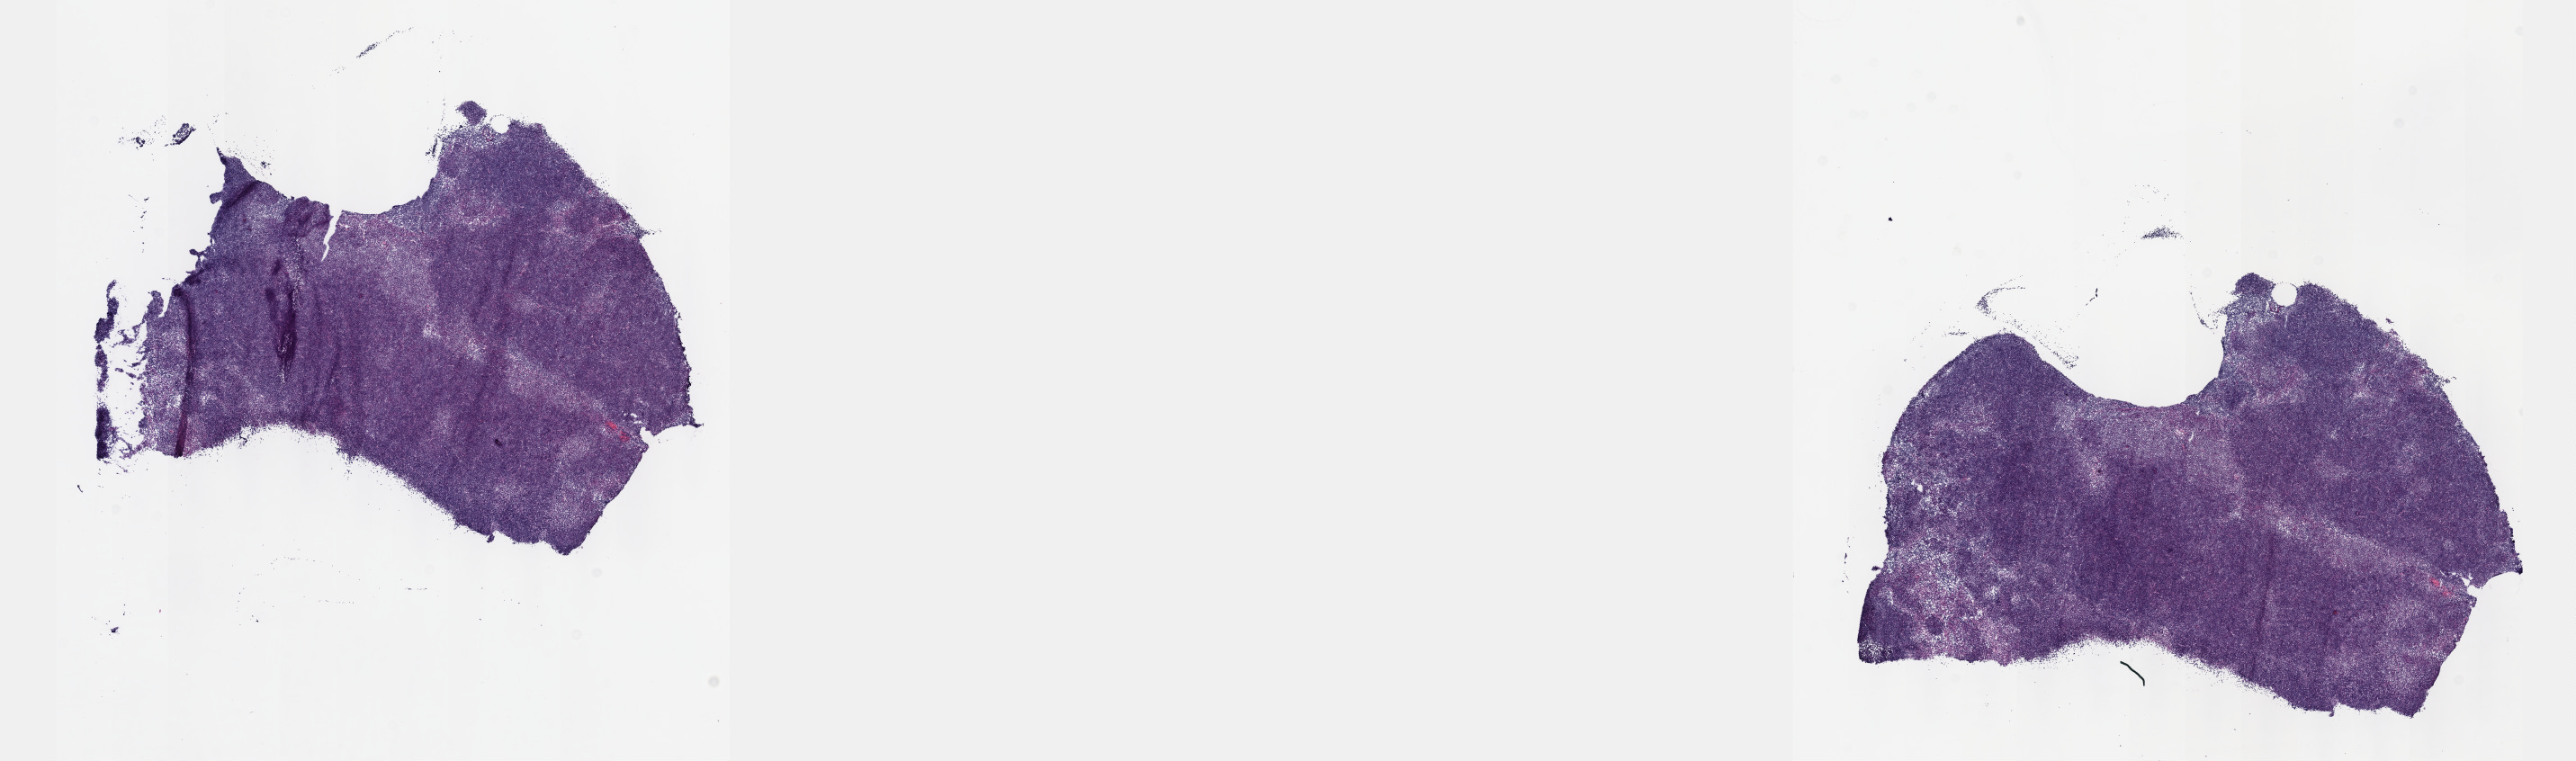
Digitized H&E-stained tissue section (whole slide) — a low-resolution overview of the entire scanned area, about 23.1 x 6.8 mm (slide scanned at 40x), frozen section from the top of the tissue portion, sample: primary tumour, thymus. Patient: male, age at initial diagnosis 51 years. Composition of this section per pathologist review: tumour cells 85%, tumour nuclei 90%, normal cells 0%, stromal cells 15%, necrosis 0%. Inflammatory infiltration, as recorded: lymphocyte infiltration 0%, monocyte infiltration 0%, neutrophil infiltration 0%.
Diagnosis: Thymoma, type B1, malignant.